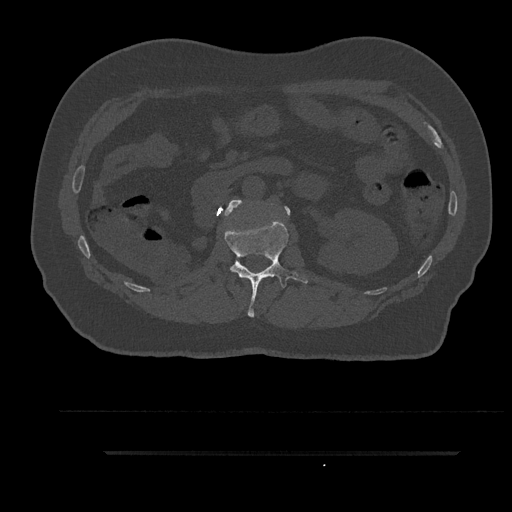
CT including the spine, one axial slice. Position 164 of 797 along the scan axis. Reconstruction kernel Br40s/3. Bone window (W 1800 / L 400 HU). 0.5 mm slice thickness. 512 × 512 image matrix. Male patient, age 63 years. From the clinical record (not read from this slice): primary cancer: renal.
Outlined on this slice (semi-automatically segmented with operator editing):
- L1 vertebra: box from (x=225, y=220) to (x=308, y=318) px
- L2 vertebra: (x=224, y=200)–(x=291, y=216)